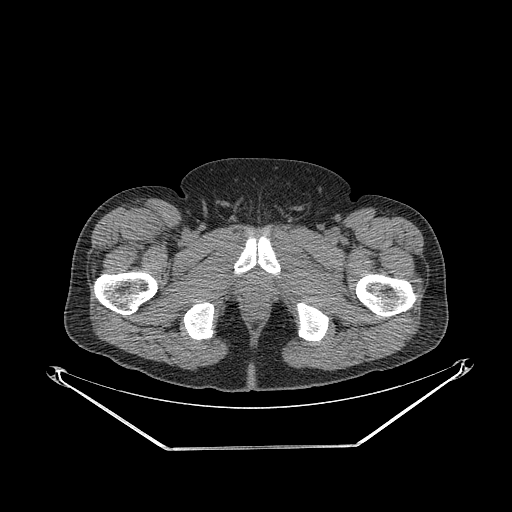
CT of an extremity soft-tissue mass (from a PET/CT study), one axial slice. Position 309 of 311 along the scan axis. Reconstruction kernel STANDARD. Soft-tissue window (W 400 / L 40 HU). 512 × 512 image matrix, field of view 500 × 500 mm. Male patient. From the clinical record (not read from this slice): histological type: pleiomorphic leiomyosarcoma; grade: intermediate; site of the primary tumour: right thigh.
Annotated regions visible in this slice (expert contour drawn on MRI and transferred to this co-registered scan by the dataset authors):
- gross tumour volume including surrounding oedema: bounding box (x1, y1, x2, y2) in pixels: (142, 210, 163, 232)